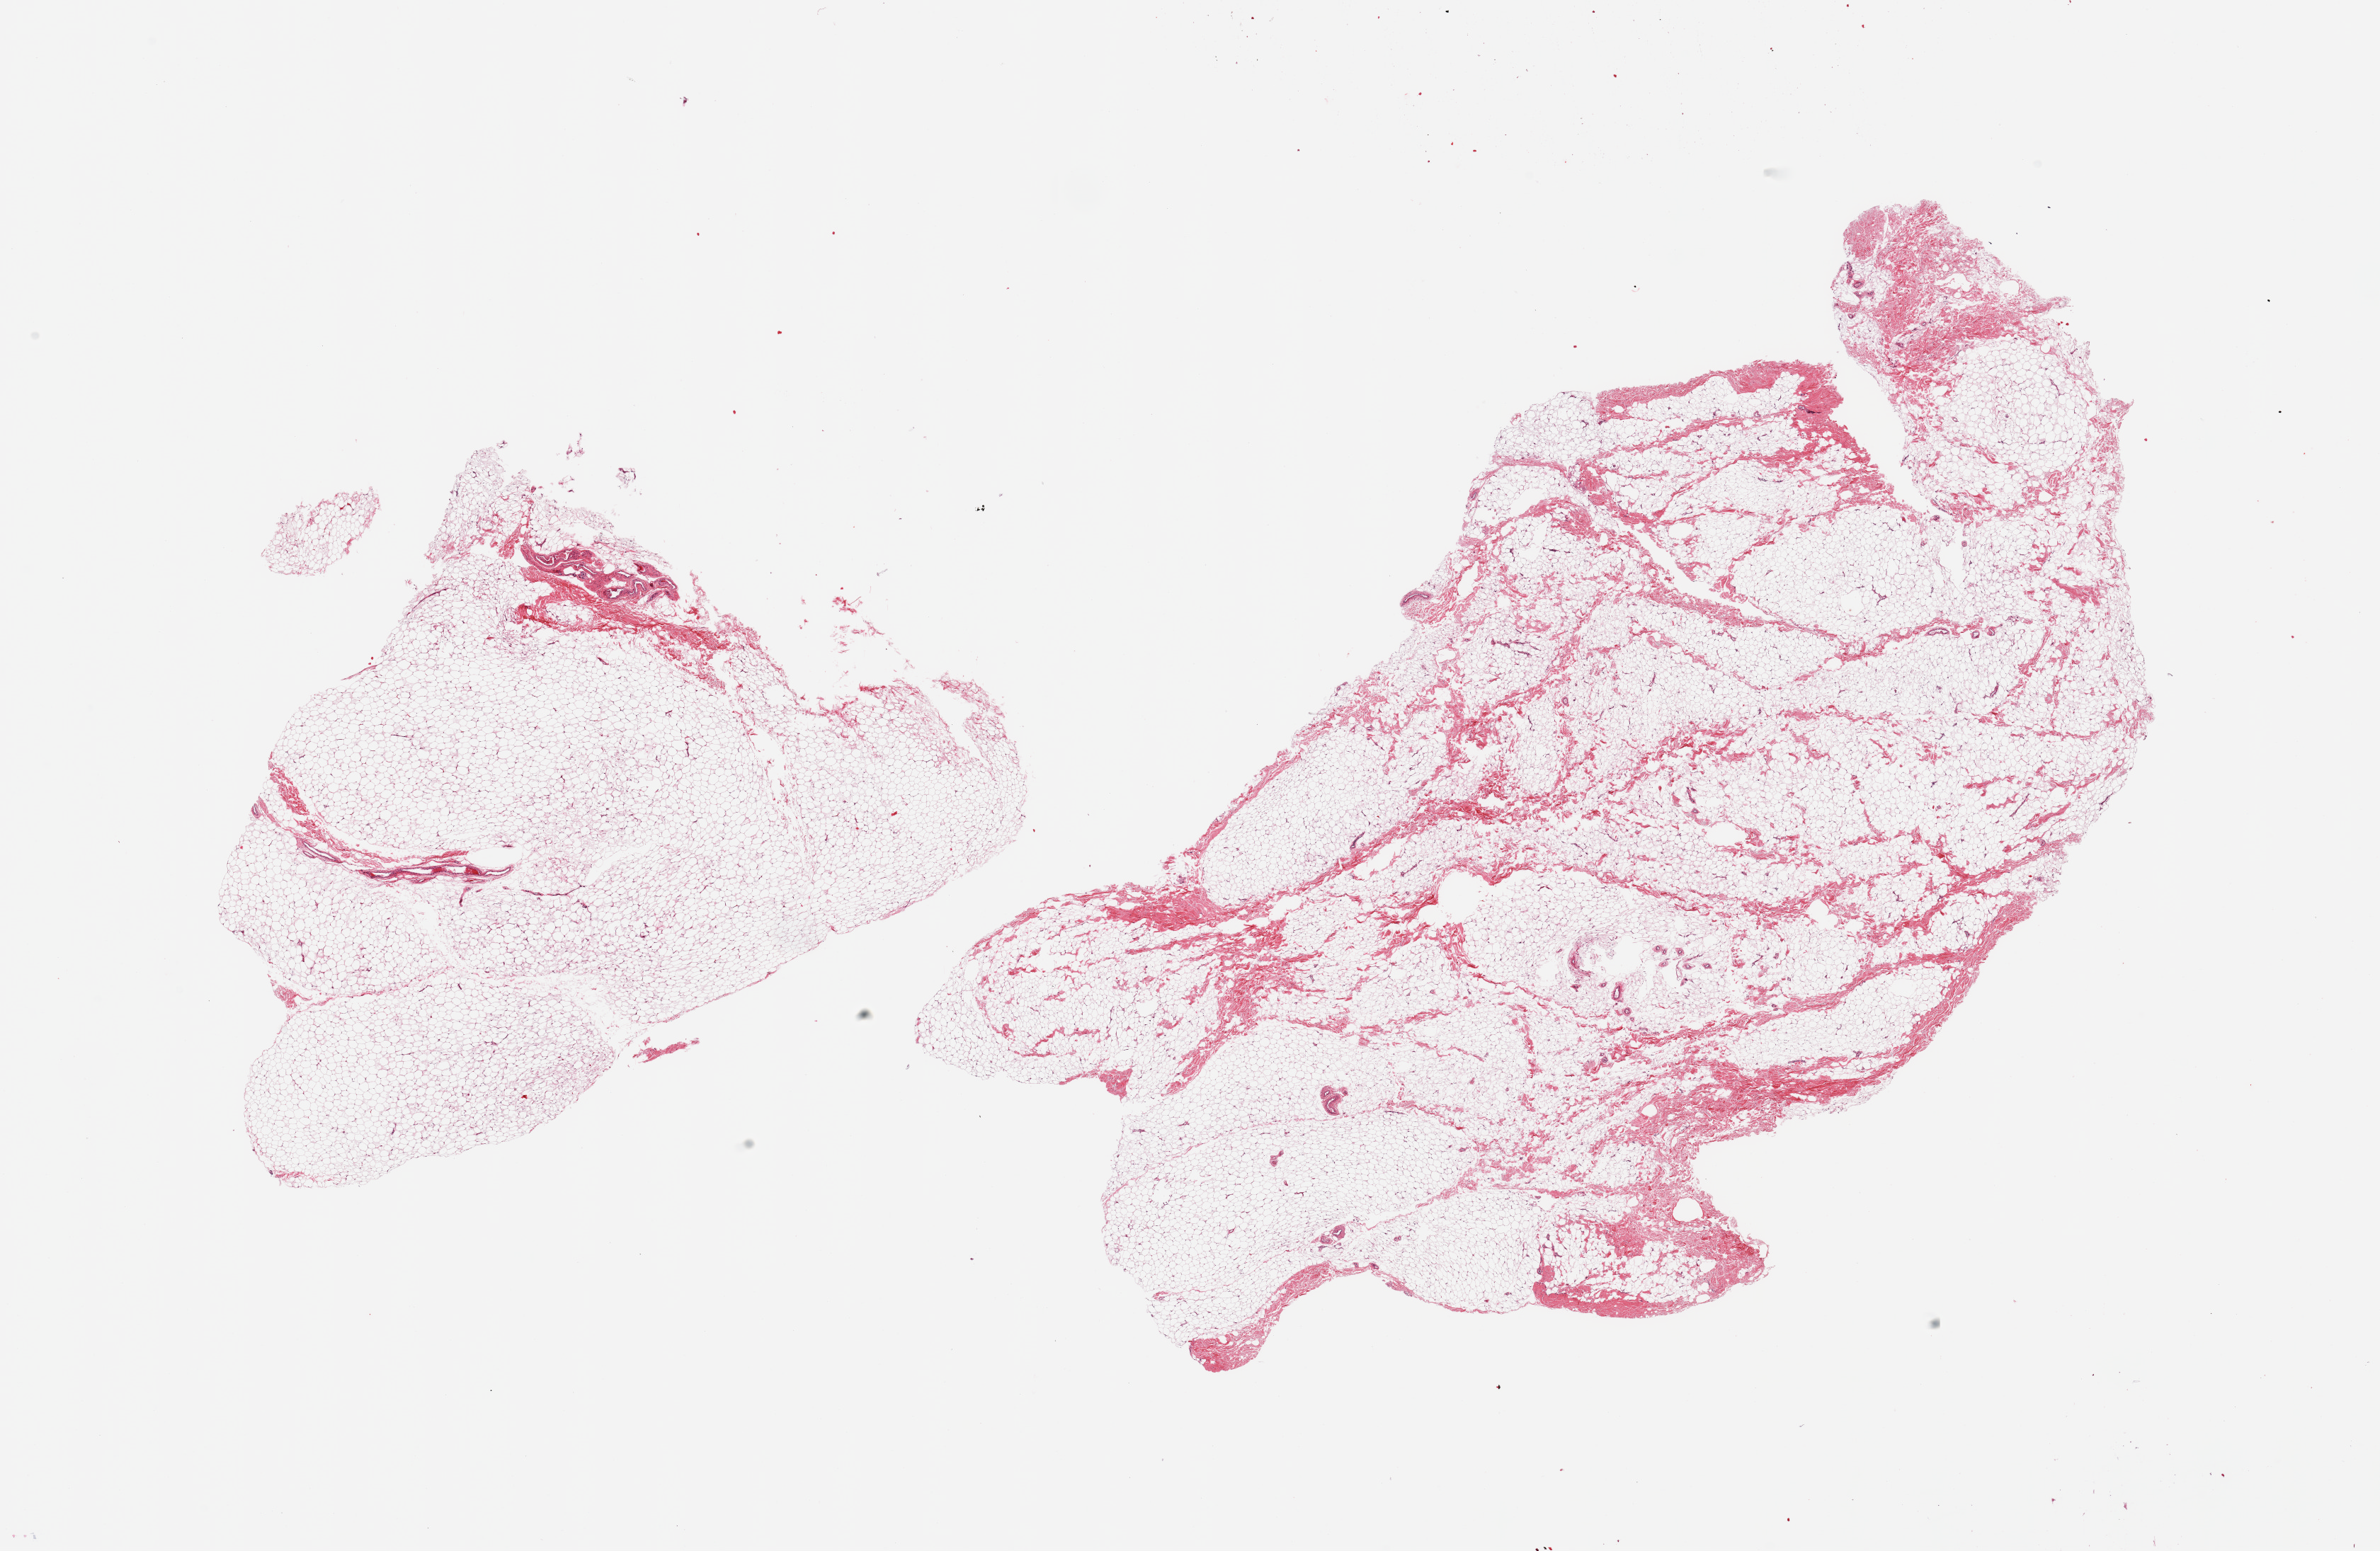
Hematoxylin and eosin (H&E) whole-slide image — a low-resolution overview of the entire scanned area, about 26.6 x 17.3 mm (slide scanned at 20x), PAXgene-fixed paraffin-embedded (PFPE) section, section of breast (target tissue), tissue donor sample. Male donor.
Review note (as recorded): 2 pieces; mainly mature adipose tissue without ductal structures; ~10% to 20% fibrovascular component.